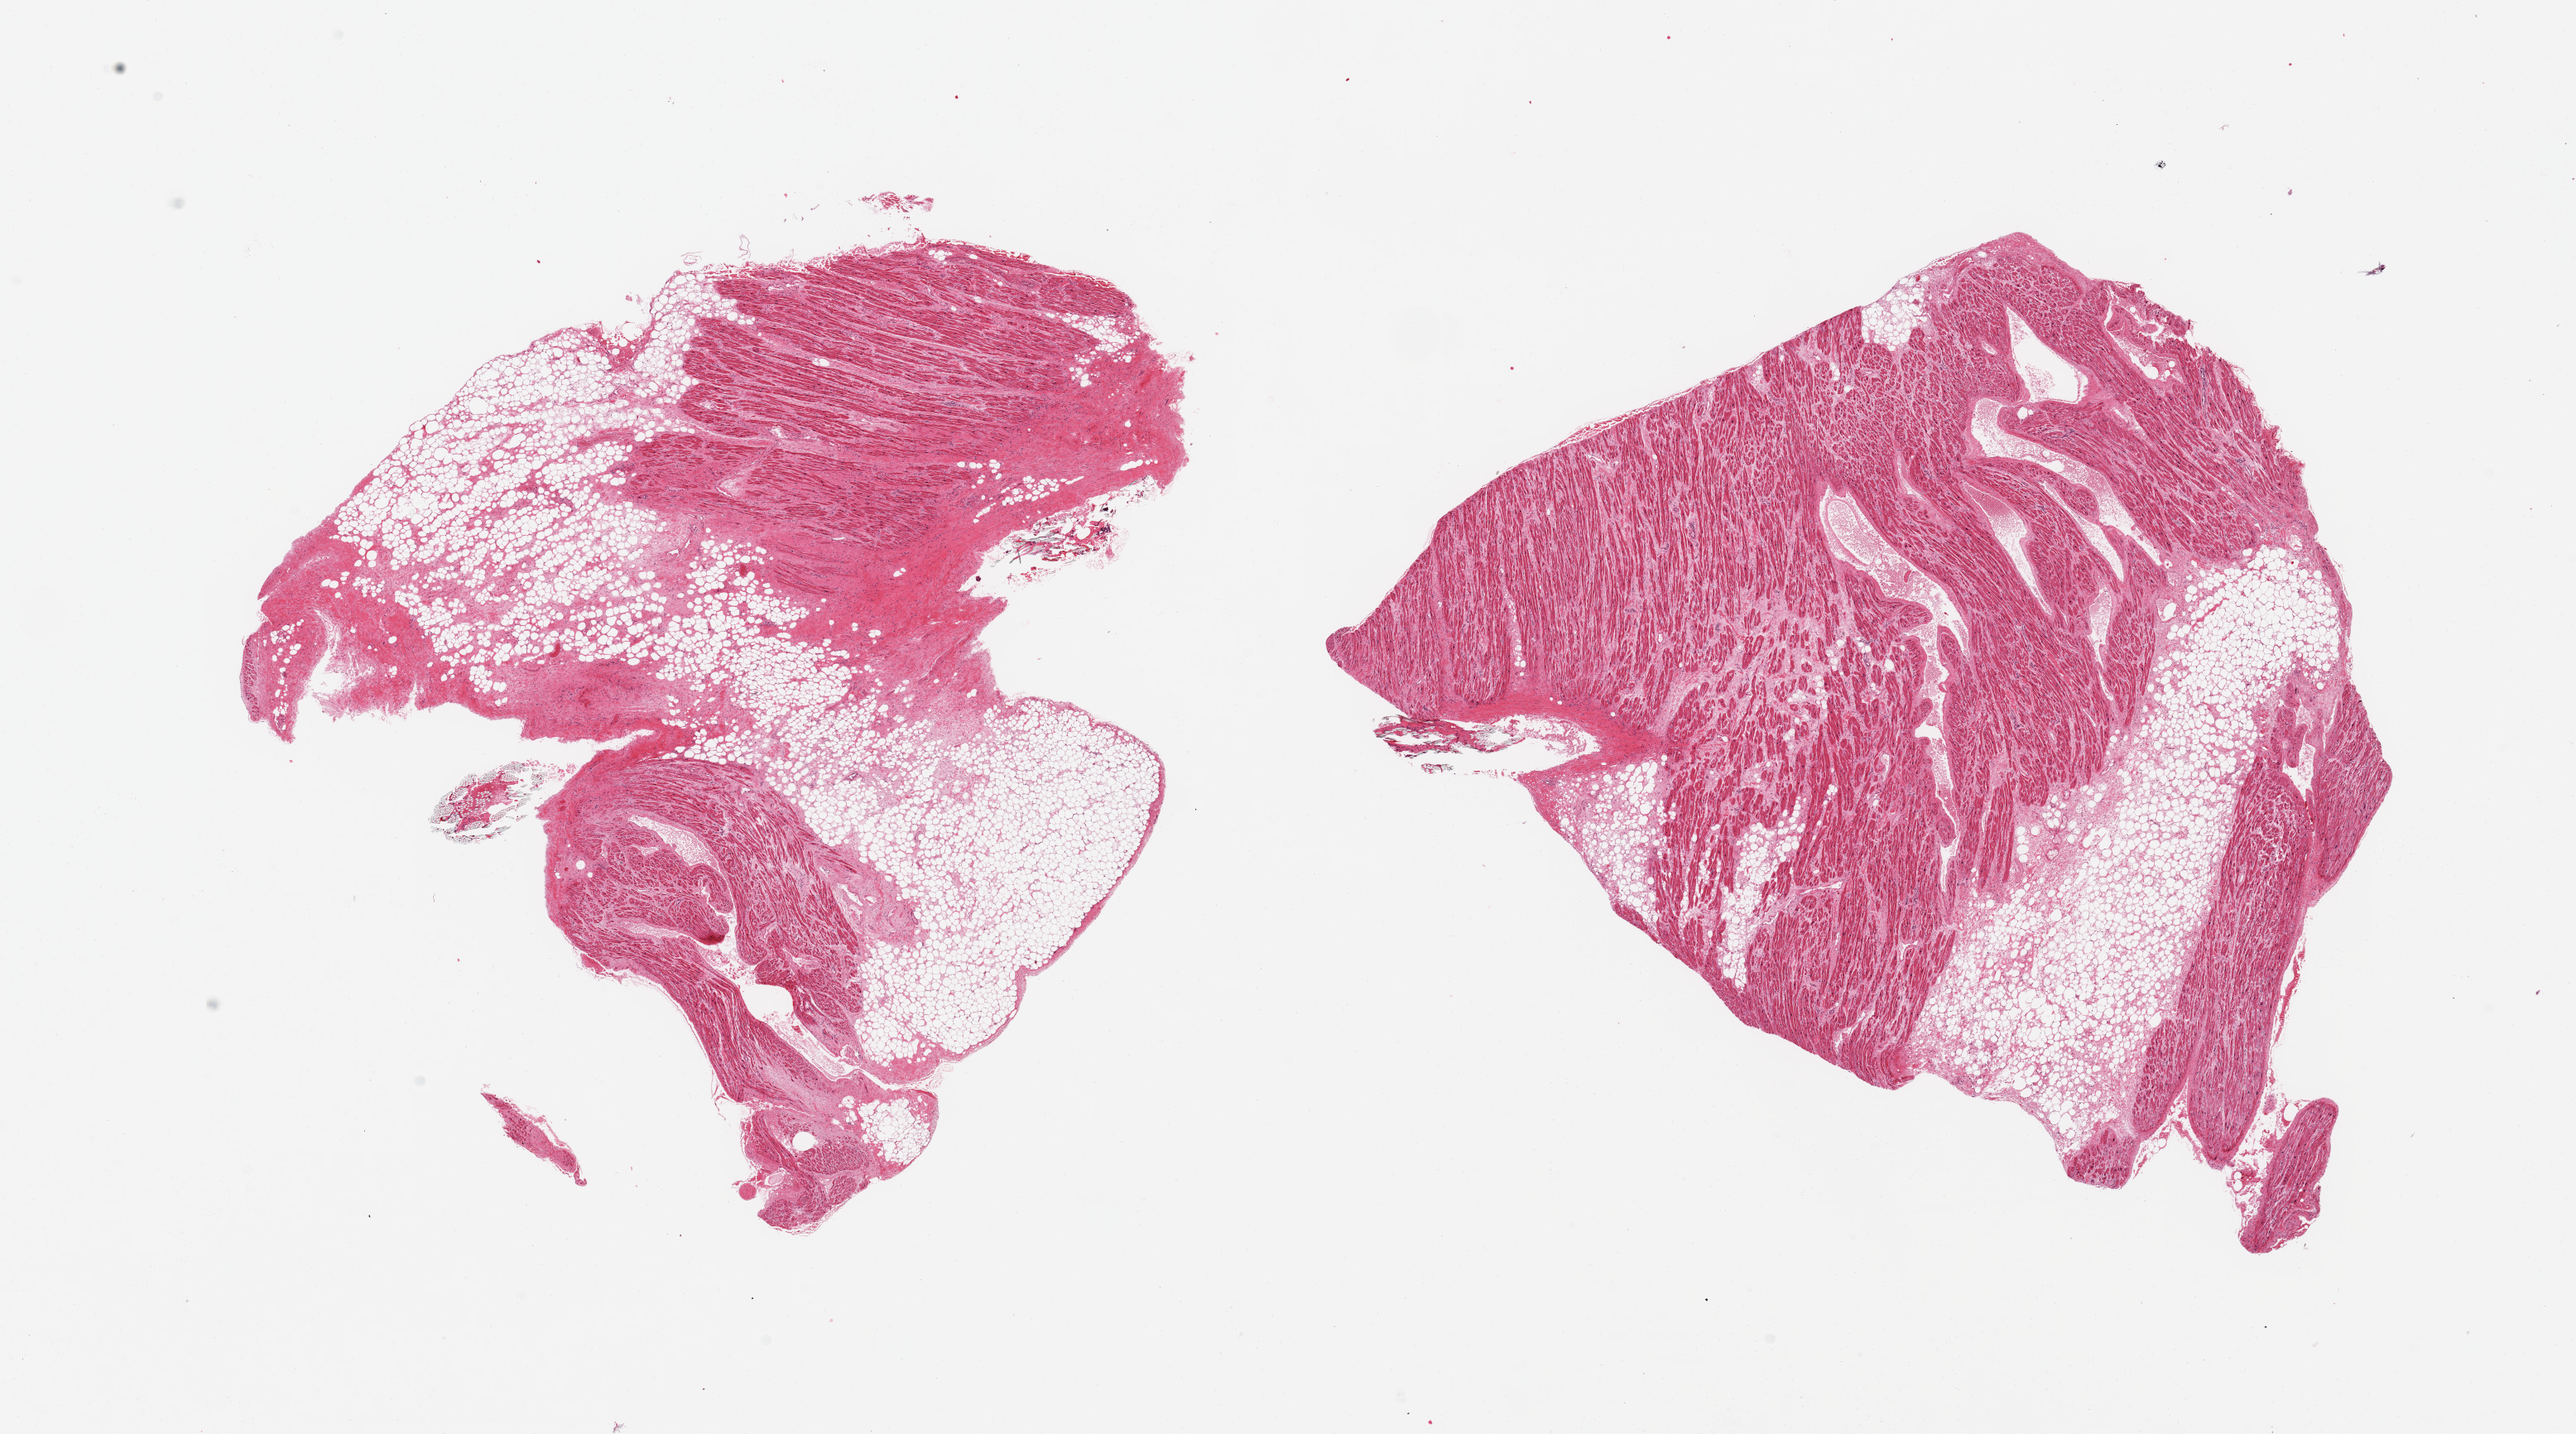
Hematoxylin and eosin (H&E) whole-slide image — shown as a low-resolution overview of the whole scanned area (about 24.6 x 13.7 mm, acquisition: 20x scan), PAXgene-fixed paraffin-embedded (PFPE) section, sampled site (target tissue): auricular appendage, donor tissue sample. Donor: male.
- review note (as recorded): 2 pieces, no abnormalities; ~40% interstitial/epicardial fat